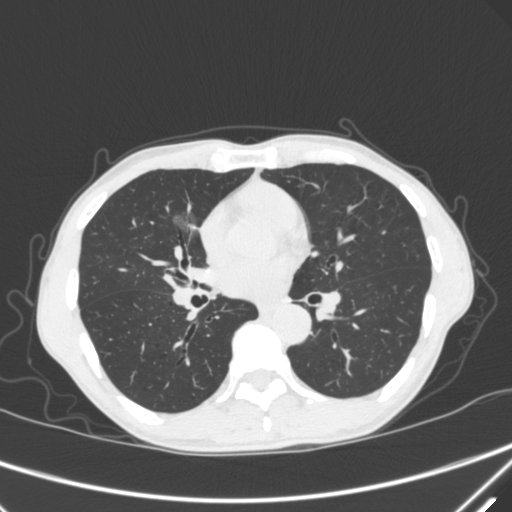
Chest CT, one axial slice; slice 170 of 340 in the series (ordered by position); lung window (W 1500 / L -600 HU); 512 × 512 image matrix, field of view 350 × 350 mm. Male patient, age 67 years. Case-level facts recorded for this patient, not image findings: clinical TNM (as recorded): T1c N0 M0; histopathological grade: G1-2.
Annotated regions visible in this slice (bounding box drawn by a radiologist):
- lung tumour (recorded histology: adenocarcinoma): box from (x=163, y=201) to (x=203, y=245) px